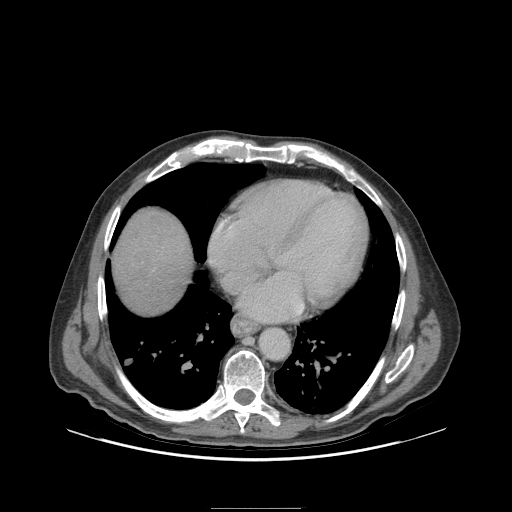
Contrast-enhanced abdominal CT (liver protocol), one axial slice; position 95 of 105 along the scan axis; reconstruction kernel STANDARD; 140 kVp; soft-tissue window (W 400 / L 40 HU); 2.5 mm slice thickness; 512 × 512 image matrix, field of view 440 × 440 mm. From the clinical record (not read from this slice): diagnosis: hepatocellular carcinoma (patient treated with transarterial chemoembolisation; whether this scan precedes or follows treatment is not stated here); TNM stage (as recorded): Stage-I; Child-Pugh class: A; tumour nodularity: uninodular; tumour size: 5.1 cm.
Outlined on this slice (semi-automatically segmented with operator editing):
- liver parenchyma outside the tumour (the mass and vessels are separate outlines, so this box may not span the whole liver): bounding box [x1, y1, x2, y2] px = [112, 208, 192, 312]